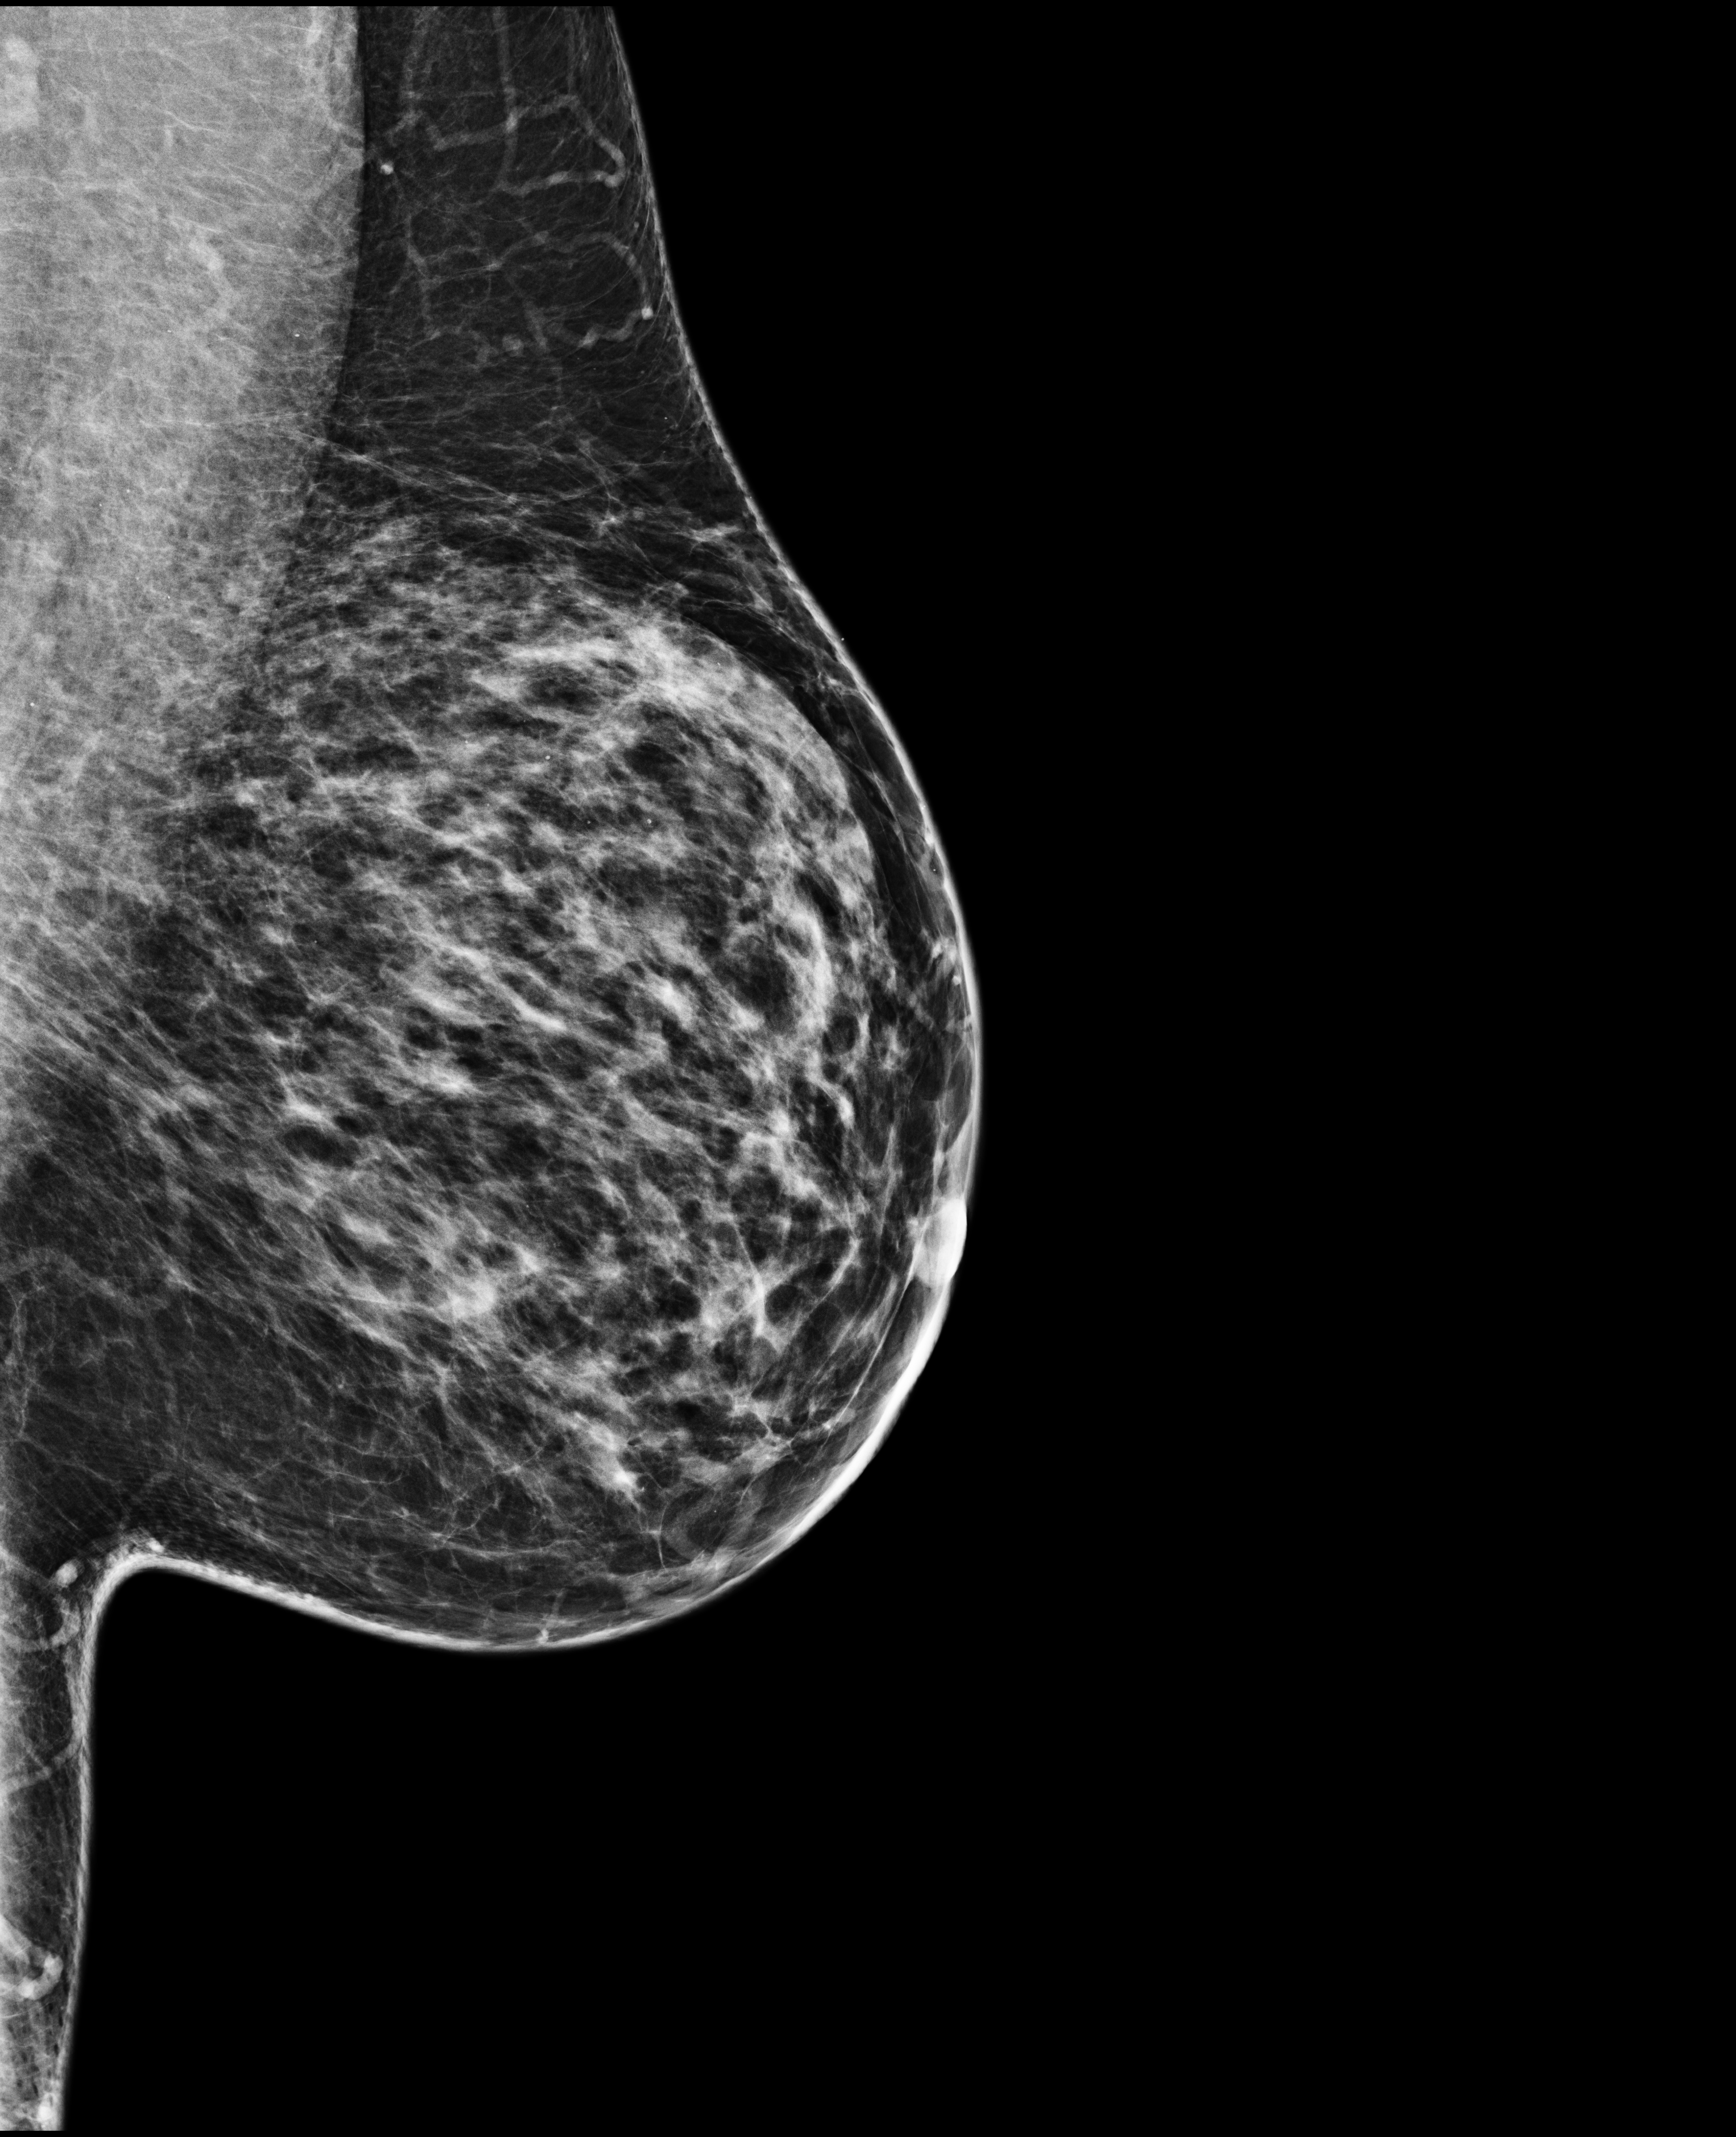
Screening examination, system: Selenia Dimensions. Patient: female, 49 years.
Image type: full-field digital mammogram. Breast: left. Projection: mediolateral oblique (MLO) view.